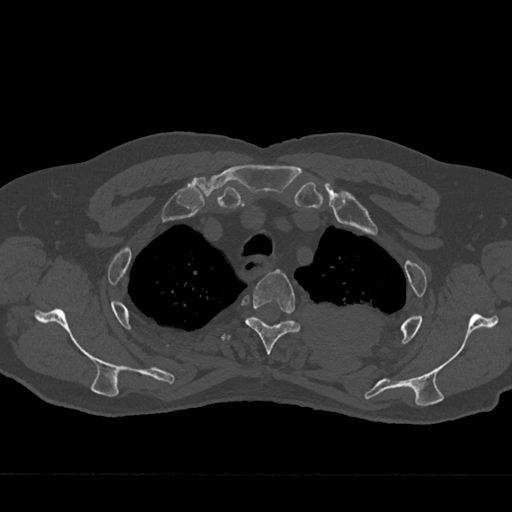
CT including the spine, one axial slice; position 565 of 797 along the scan axis; reconstruction kernel Br40s/3; 120 kVp; bone window (W 1800 / L 400 HU); 0.5 mm slice thickness; 512 × 512 image matrix, field of view 377 × 377 mm. Patient: male, 75 years. From the clinical record (not read from this slice): primary cancer: renal; vertebrae with lytic lesions (as recorded): T4.
Outlined on this slice (semi-automatic segmentation, software-assisted and operator-edited):
- T3 vertebra: bounding box <245,269,301,355> (left, top, right, bottom; pixels)
- T4 vertebra: <227,336,231,340>